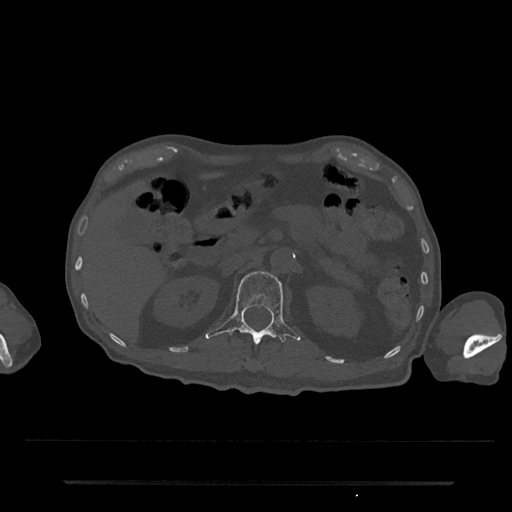
CT including the spine, one axial slice; position 135 of 797 along the scan axis; bone window (W 1800 / L 400 HU); 0.5 mm slice thickness; 512 × 512 image matrix. Patient: male, 74 years. Case-level facts recorded for this patient, not image findings: primary cancer: prostate.
Structures marked on this image (semi-automatically segmented with operator editing):
- L1 vertebra: box from (x=205, y=271) to (x=301, y=344) px